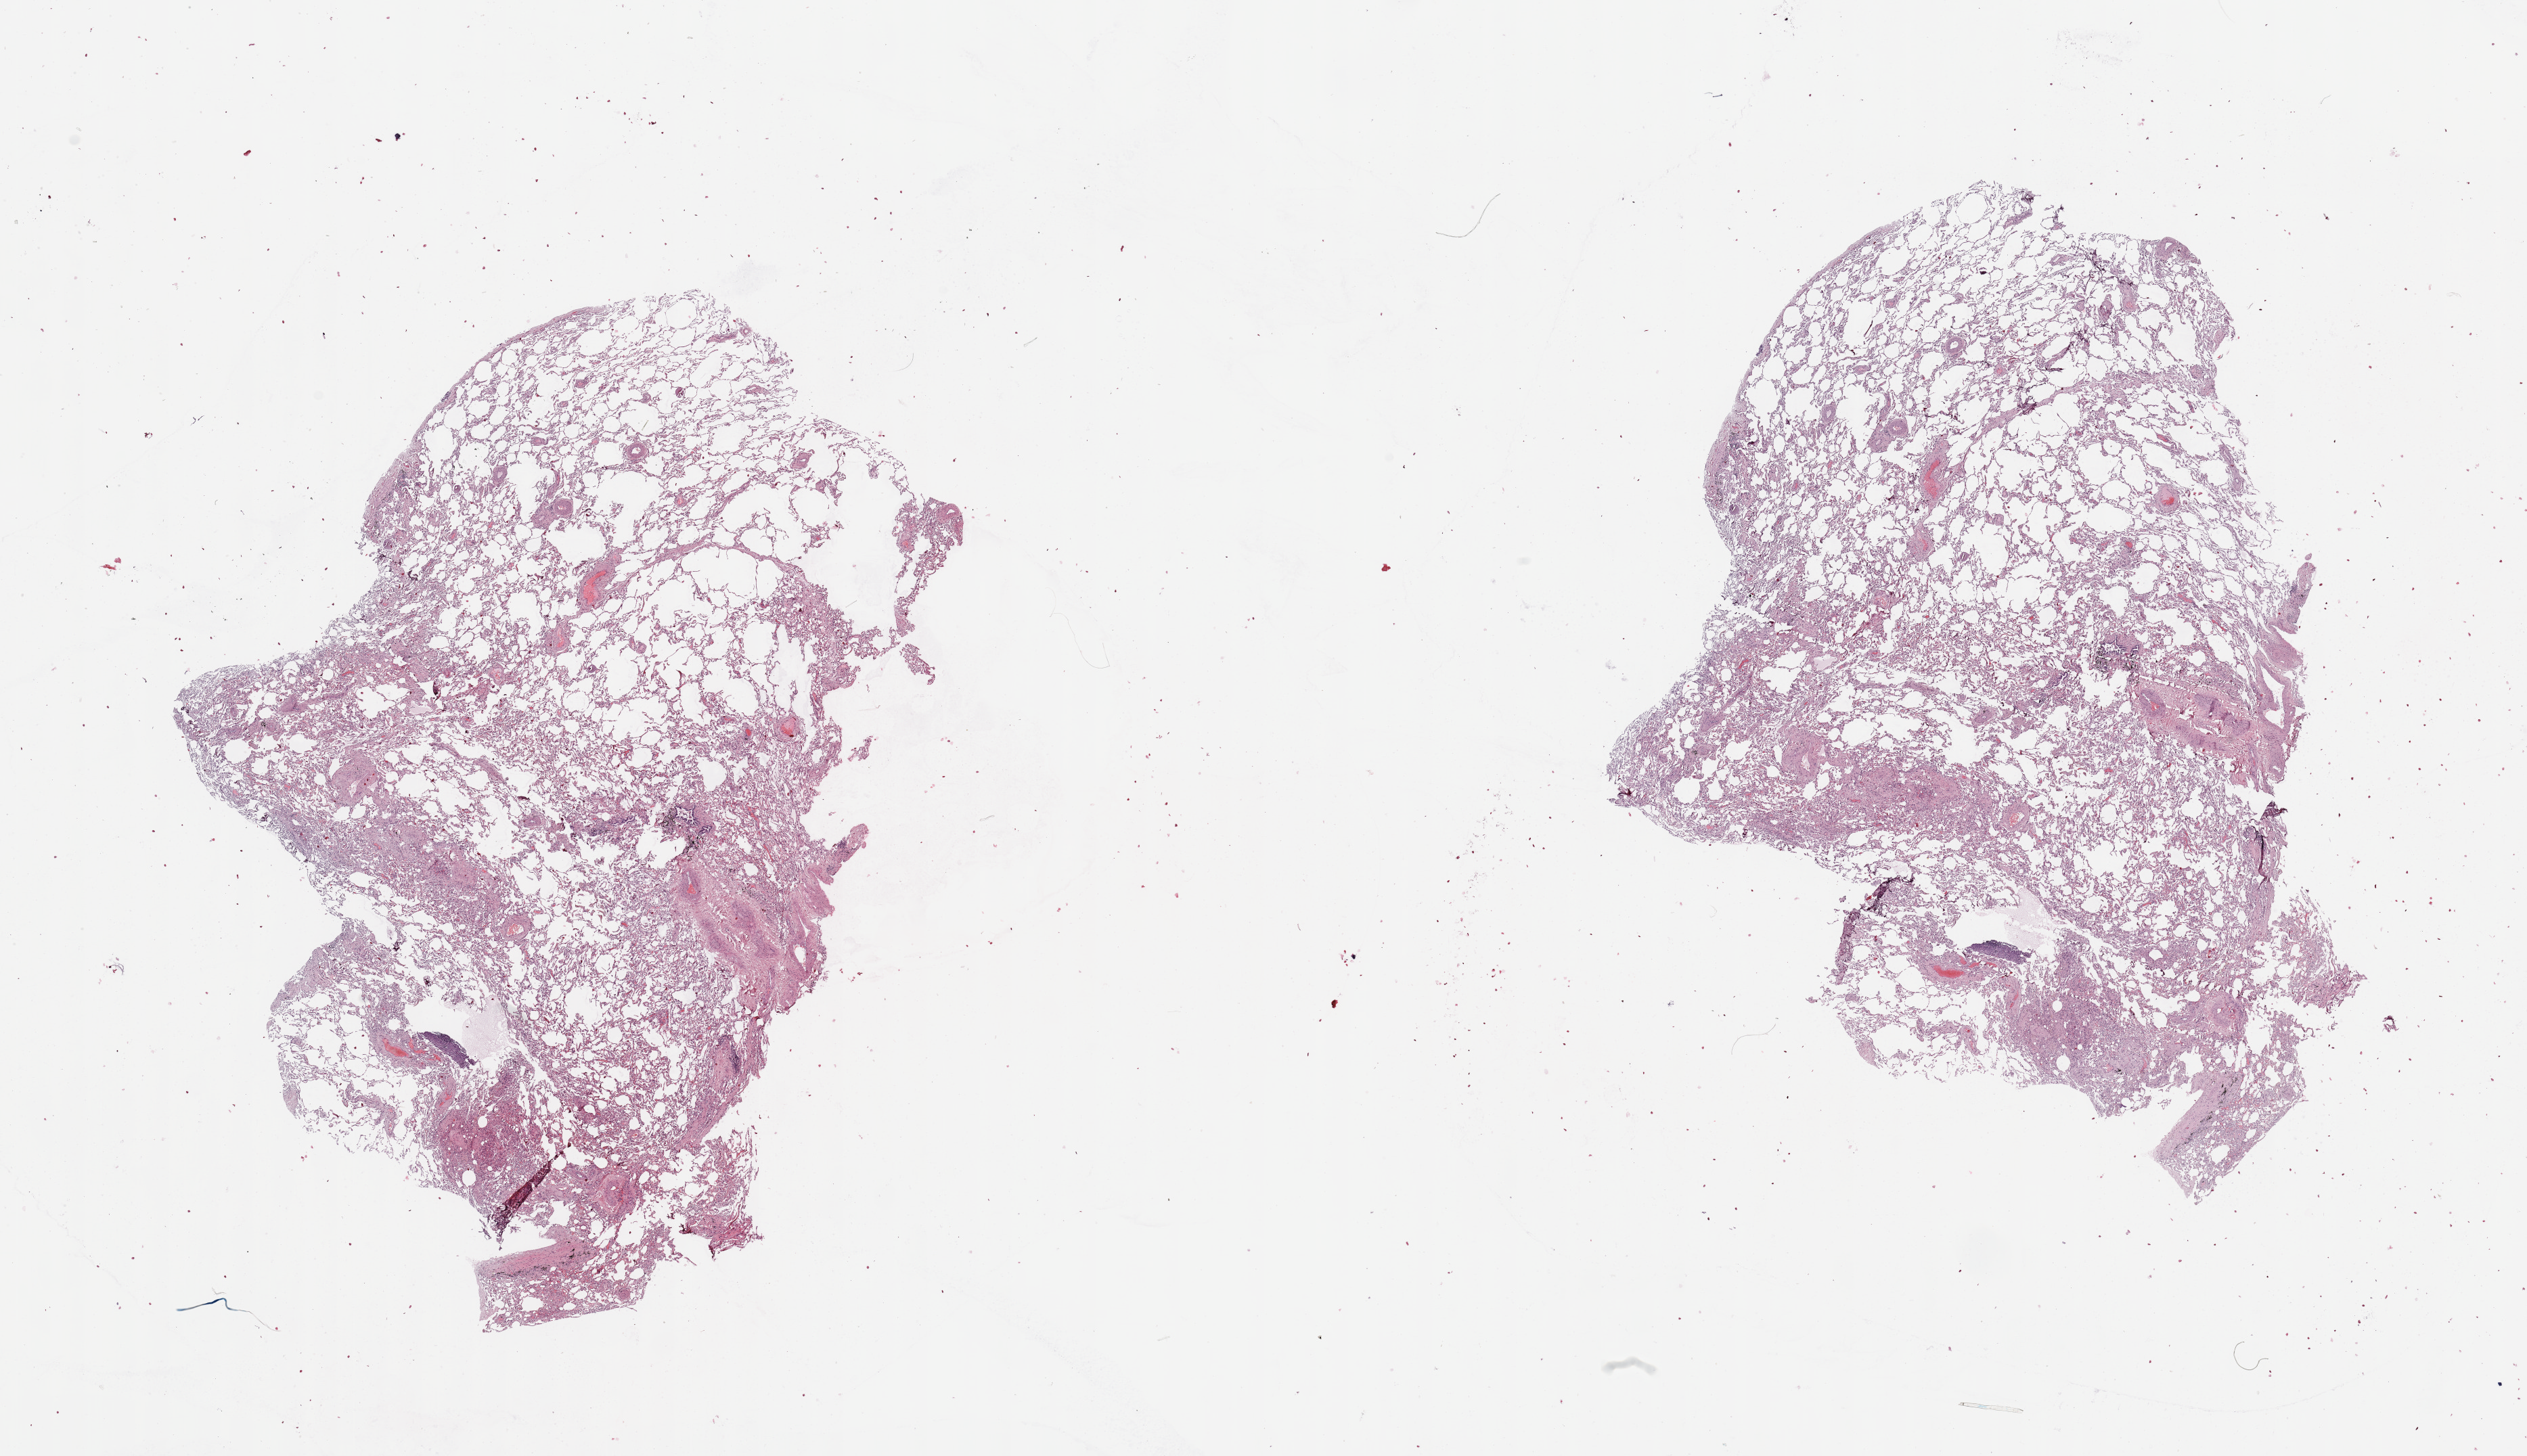
Whole-slide histology image, Hematoxylin and eosin (H&E) stained, low-resolution overview of the scanned area, about 29.5 x 17.0 mm; normal (non-tumour) tissue sample, sampled site: lung. 66-year-old male patient.
This section: normal (non-tumour) tissue from the same patient. Patient diagnosis: Squamous cell carcinoma, NOS.